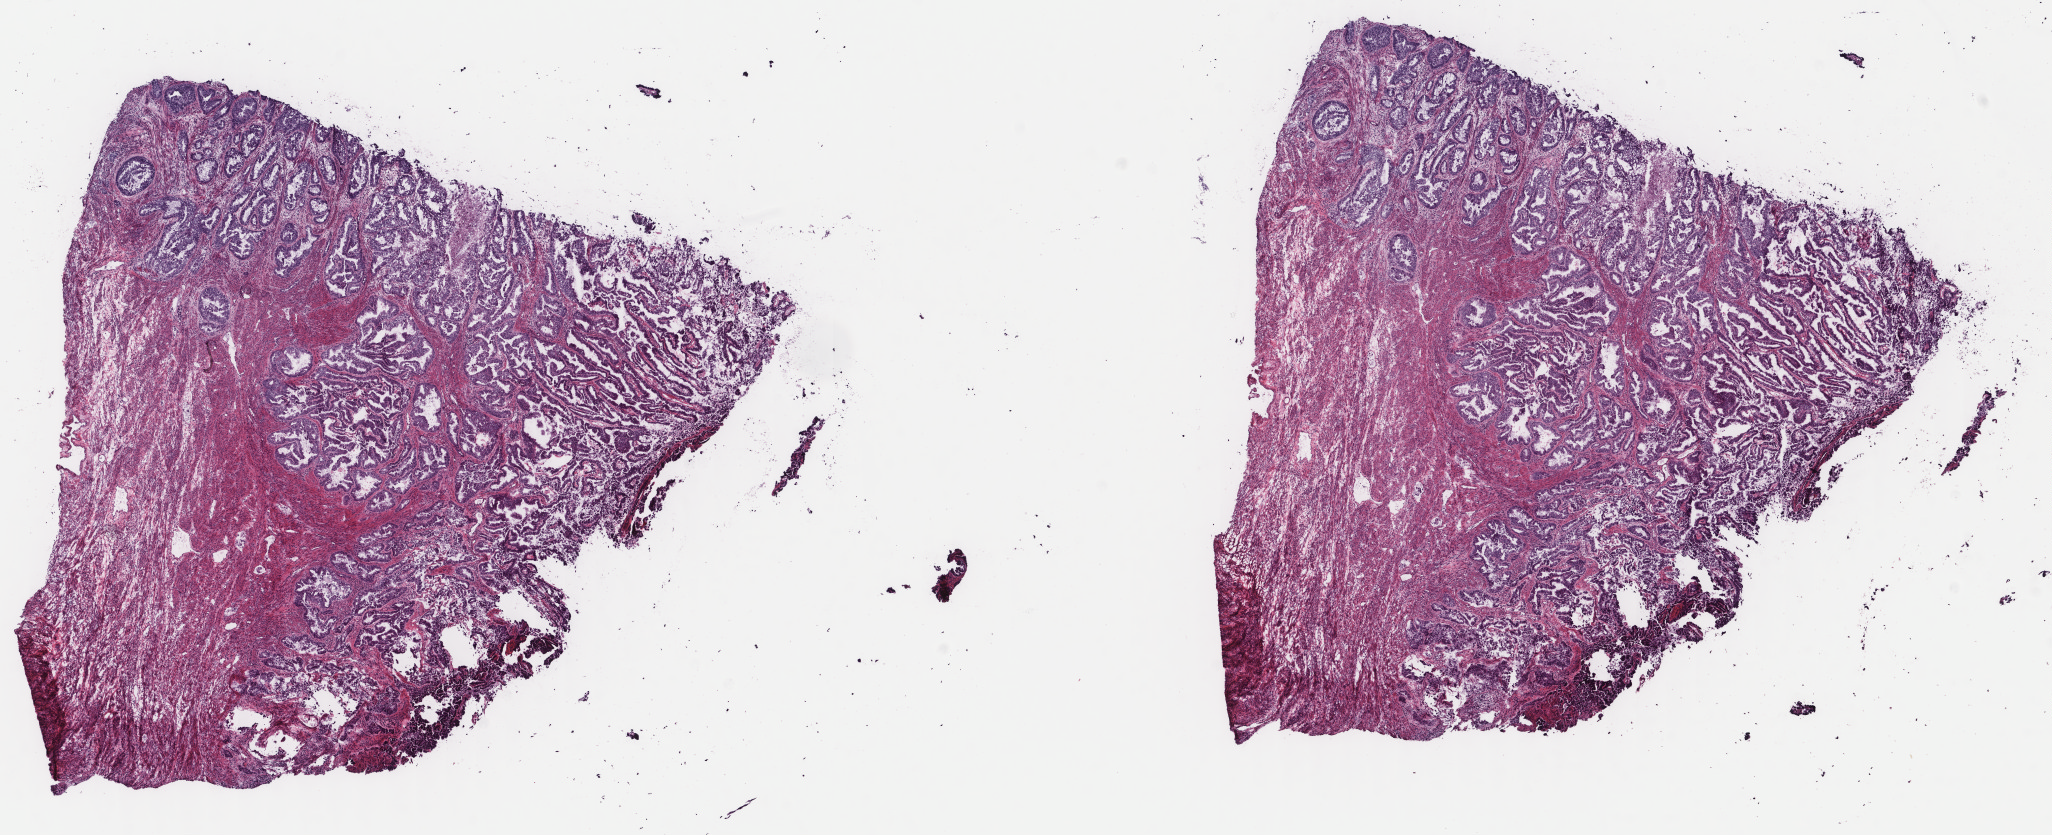
H&E-stained whole-slide image — shown as a low-resolution overview of the whole scanned area (about 16.3 x 6.6 mm), frozen section, primary tumour sample from the uterus. Patient sex: female. Histologic grade: G2 (moderately differentiated). Pathologist review of this section (percent, as recorded): tumour cells 30%, tumour nuclei 30%, normal cells 0%, stromal cells 67%, necrosis 3%. Inflammatory infiltration, as recorded: lymphocyte infiltration 8%, monocyte infiltration 0%, neutrophil infiltration 2%.
* histologic diagnosis: Endometrioid adenocarcinoma, NOS (endometrium)
* FIGO stage: IB